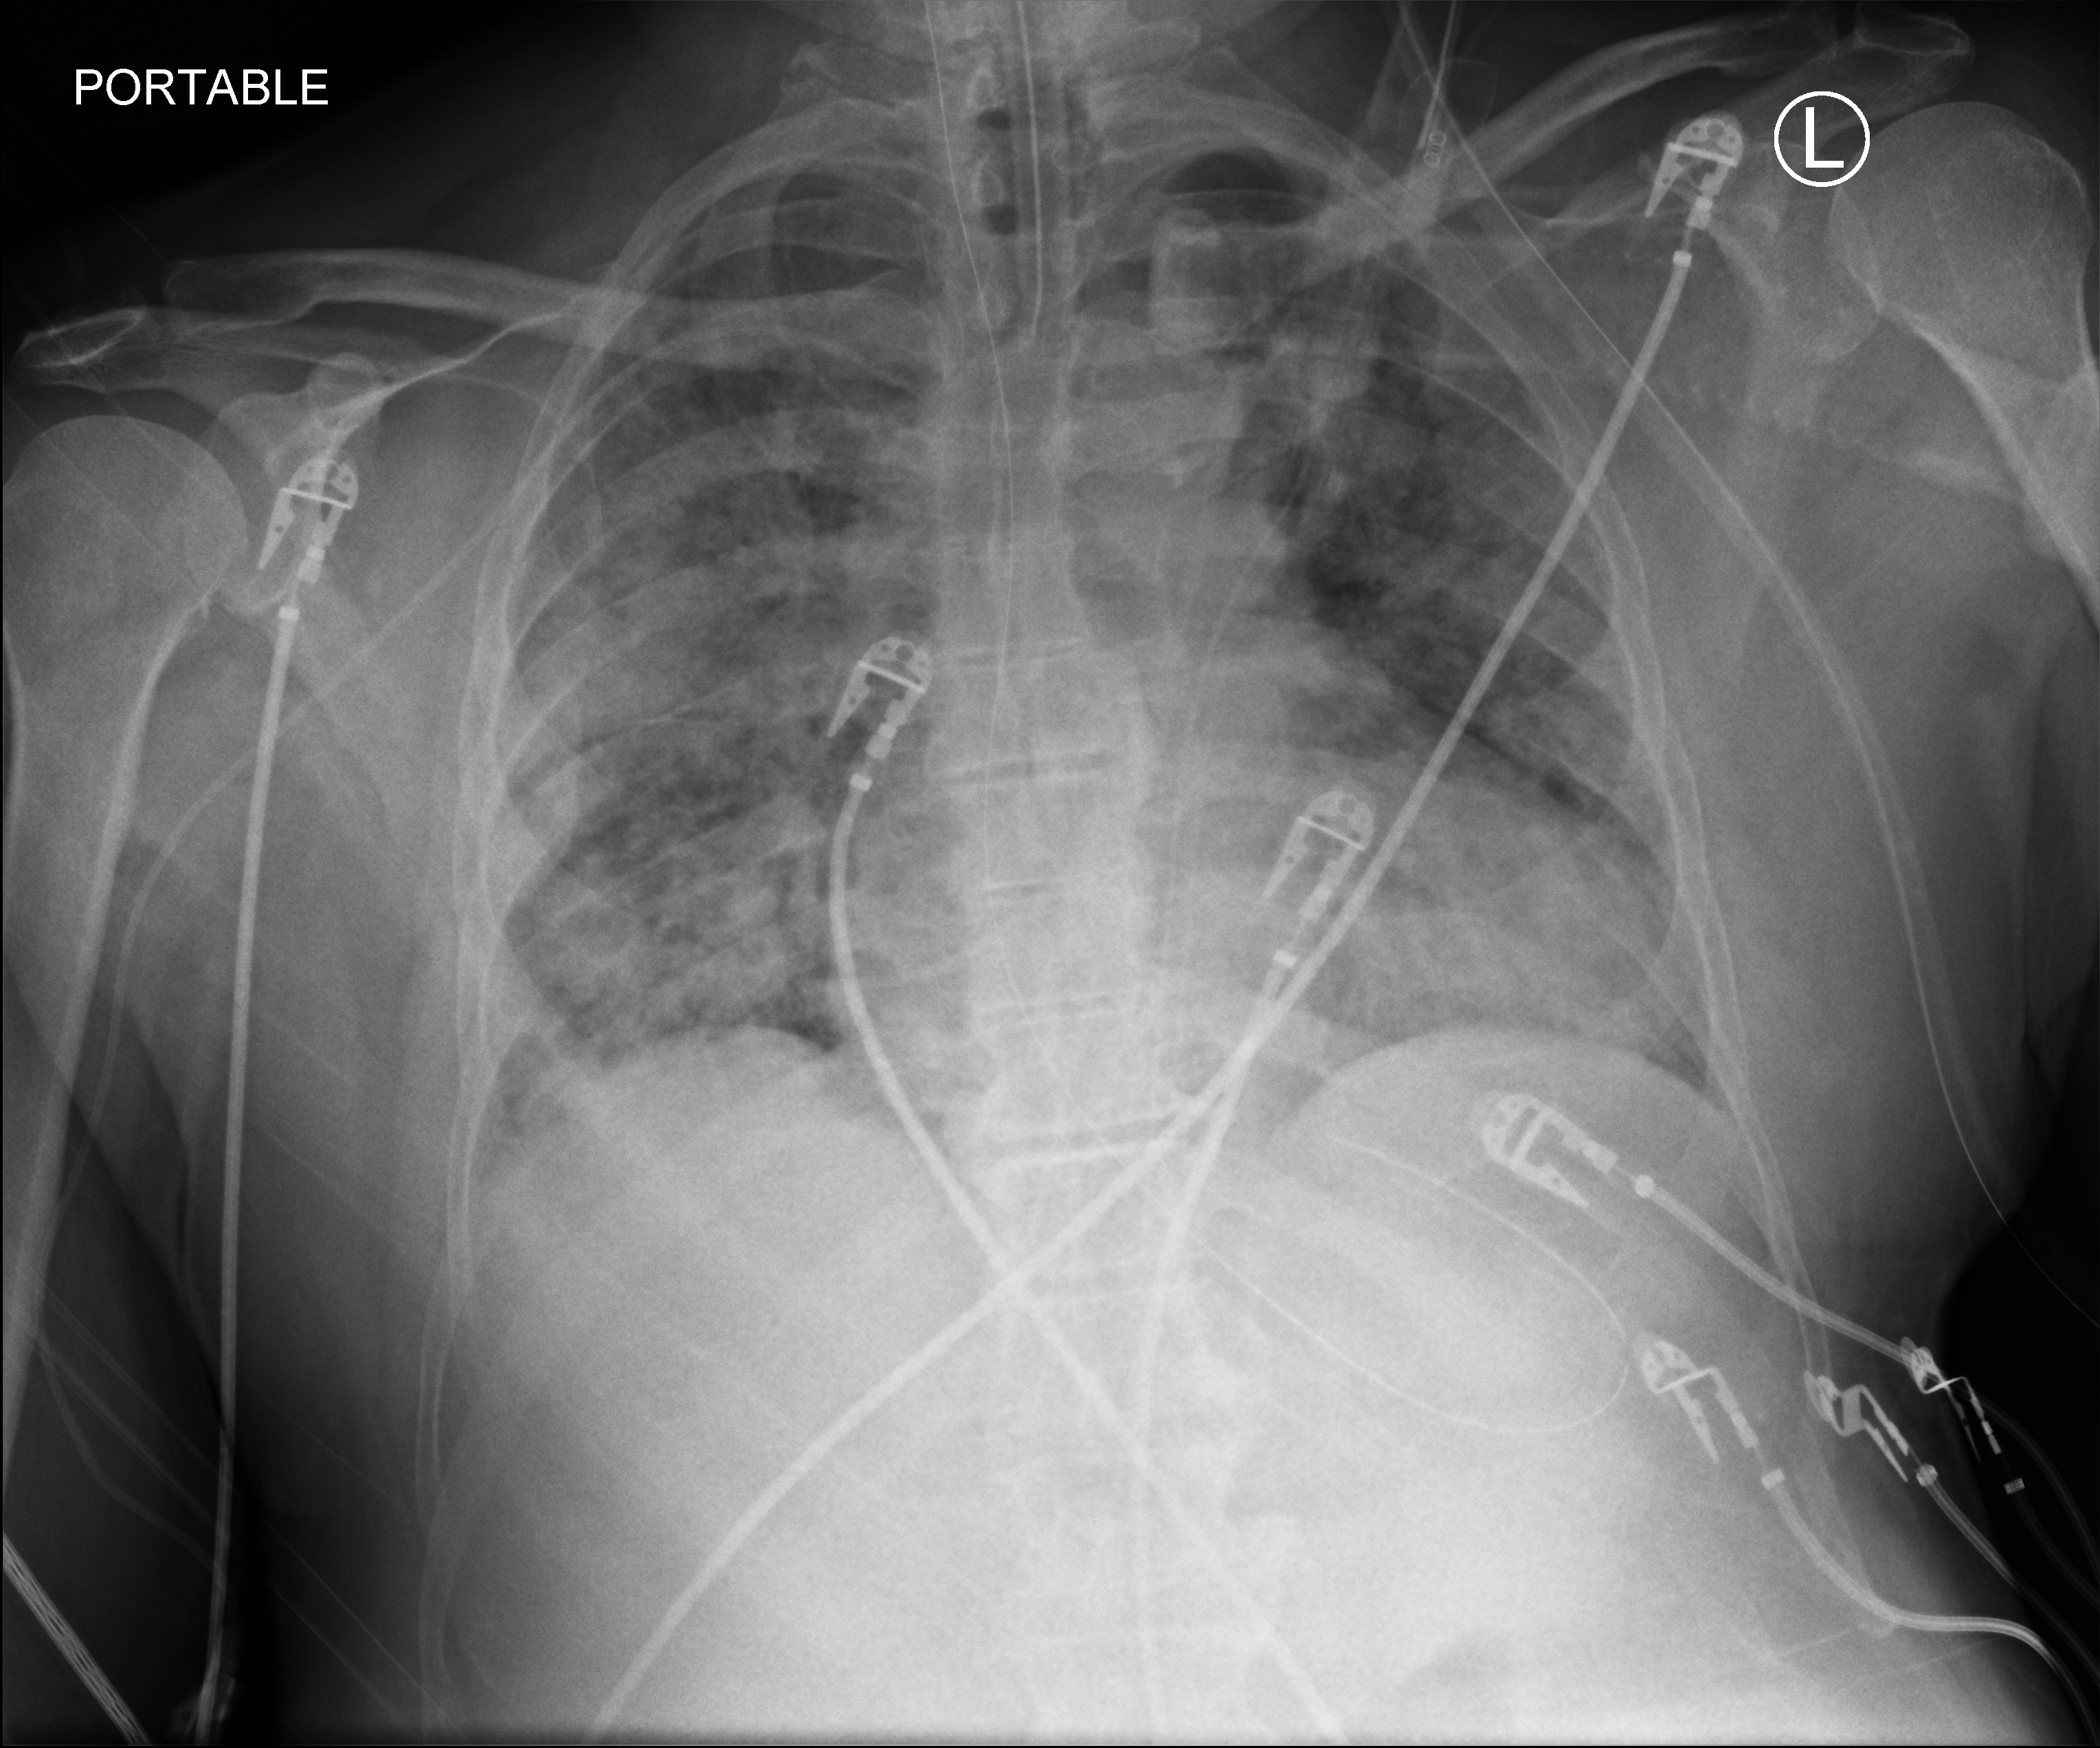
Portable chest radiograph, anteroposterior (AP) projection. Patient hospitalised with COVID-19; male, aged 60–74 years.
Hospital-stay facts (about this admission, not read from this image; timing relative to this image not recorded): admitted to intensive care during this hospital stay: yes; length of hospital stay: 31 days; mechanically ventilated during this hospital stay: yes.